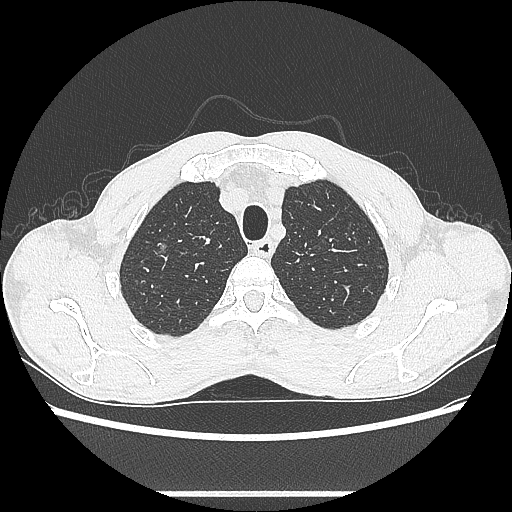
Chest CT, one axial slice. Slice 499 of 601 in the series (ordered by position). 100 kVp. Lung window (W 1500 / L -600 HU). 0.62 mm slice thickness. 512 × 512 image matrix, field of view 357 × 357 mm. Male patient, age 54 years. Case-level facts recorded for this patient, not image findings: clinical TNM (as recorded): T1a N0 M0.
Structures marked on this image (bounding box drawn by a radiologist):
- lung tumour (recorded histology: adenocarcinoma): bounding box (x1, y1, x2, y2) in pixels: (146, 237, 173, 265)